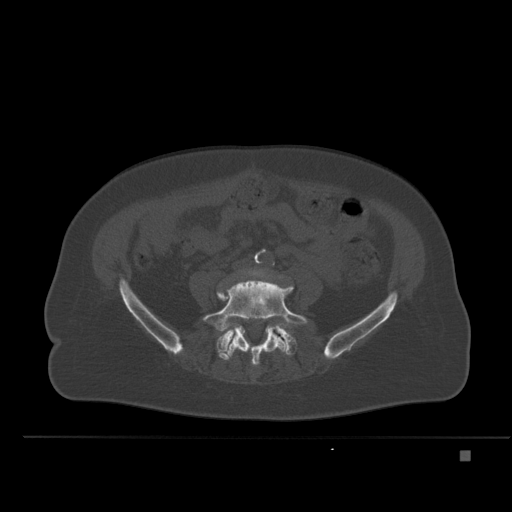
CT including the spine, one axial slice. Position 162 of 477 along the scan axis. Bone window (W 1800 / L 400 HU). 512 × 512 image matrix, field of view 422 × 422 mm. Female patient, age 74 years. Case-level facts recorded for this patient, not image findings: primary cancer: colon.
Annotated regions visible in this slice (semi-automatically segmented with operator editing):
- L4 vertebra: bounding box [x1, y1, x2, y2] px = [217, 269, 283, 296]
- L5 vertebra: [202, 277, 309, 366]